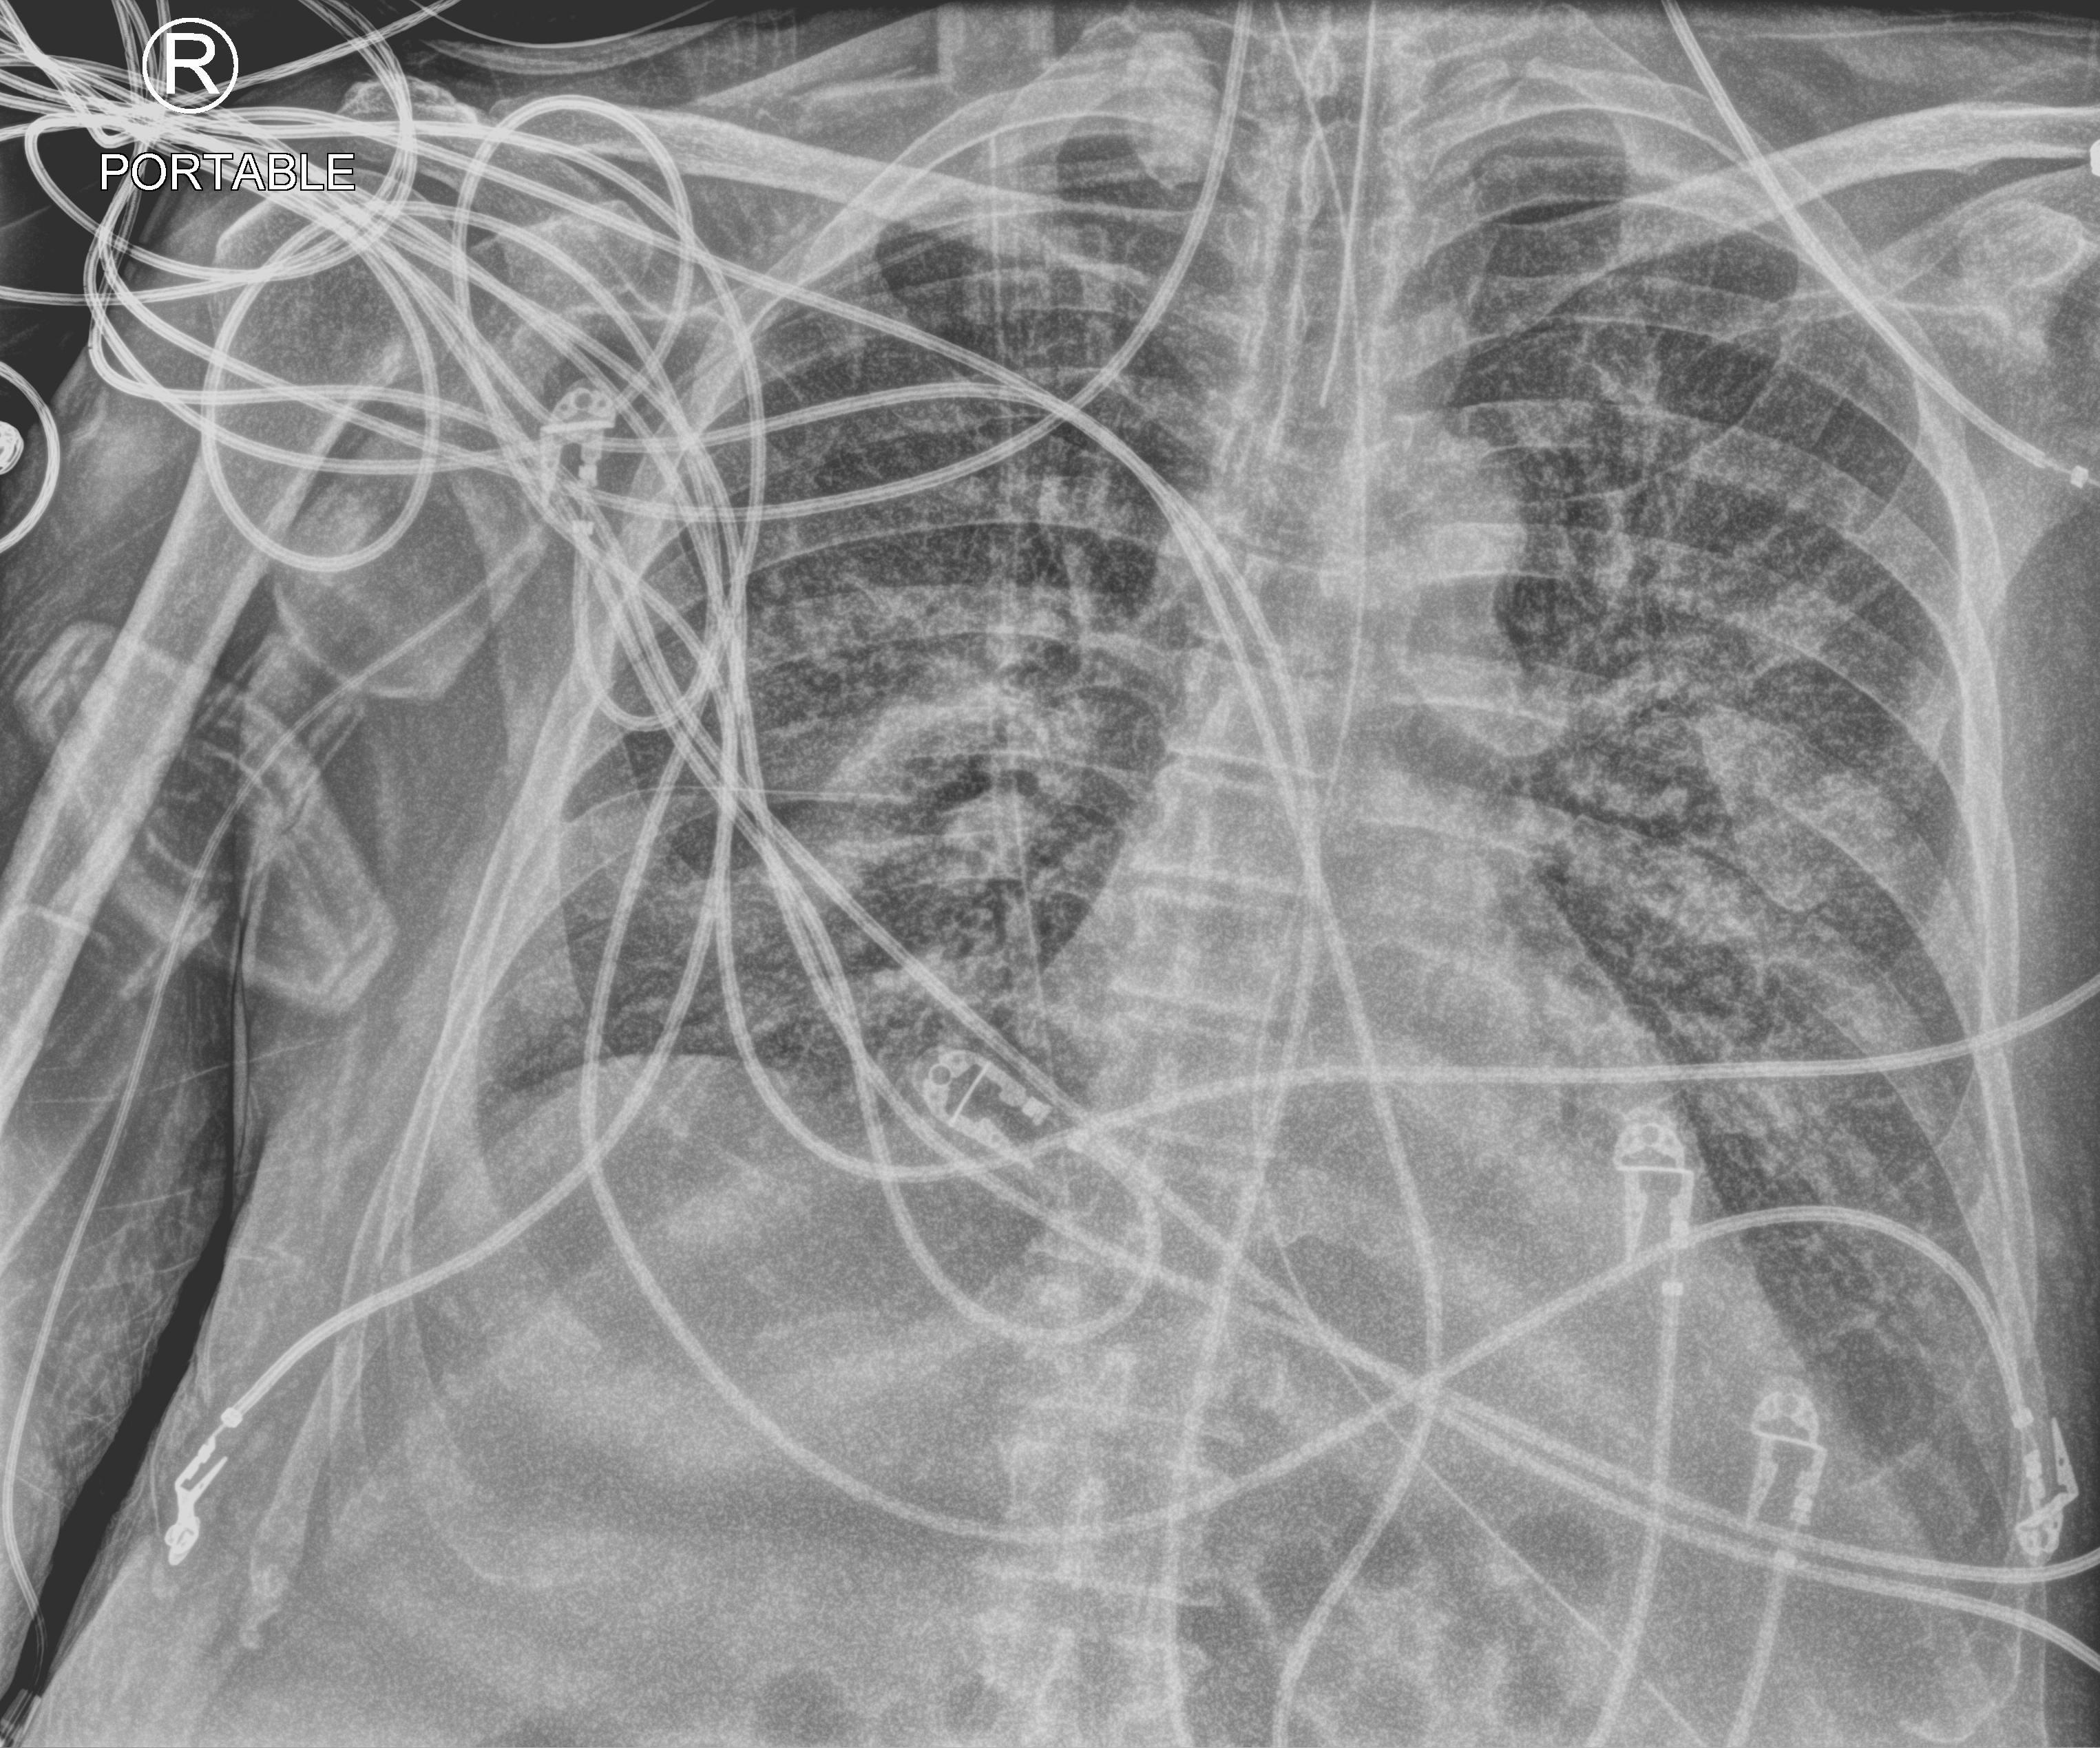
Bedside chest radiograph (computed radiography). Male patient hospitalised with COVID-19, age 60–74 years.
Admission-level facts for this patient (not findings on this image; timing relative to this image not recorded): mechanically ventilated during this hospital stay: yes.